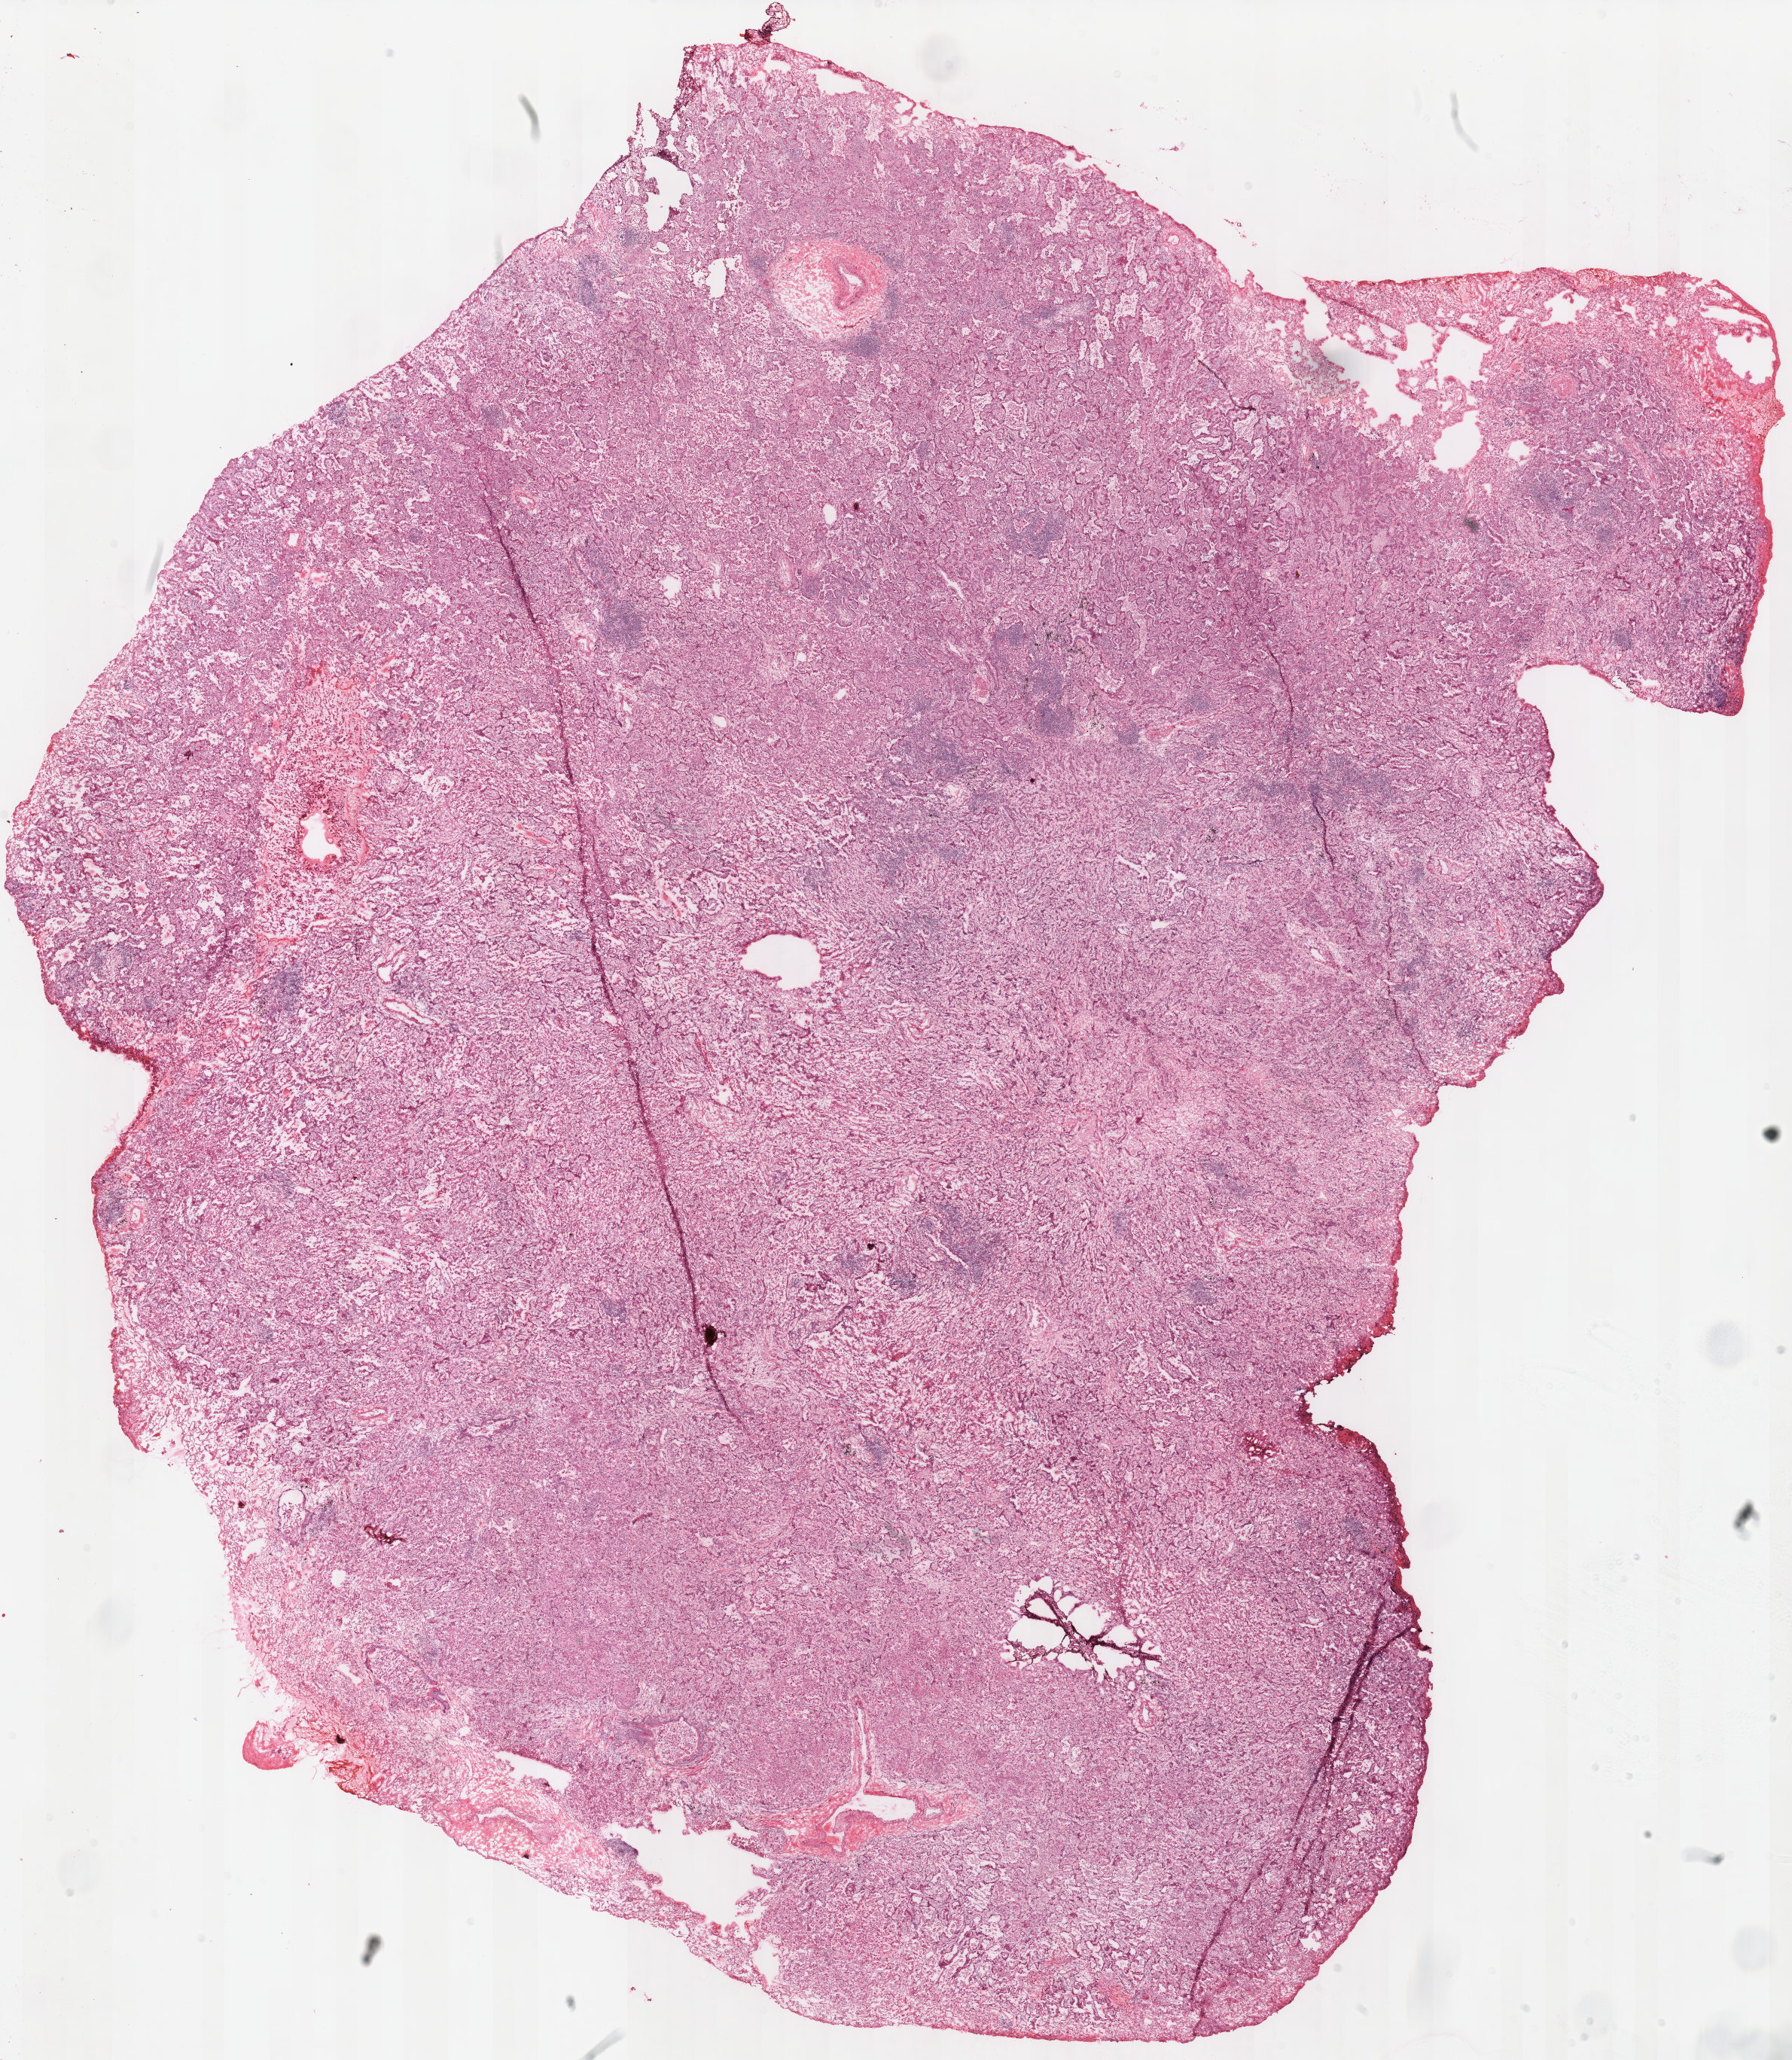
Hematoxylin and eosin (H&E) stained whole-slide image — whole scanned area (about 18.8 x 21.6 mm, slide scanned at 40x) shown as a low-resolution overview. Frozen section from the top of the tissue portion. Lung, primary tumour sample. Patient: female, age at initial diagnosis 61 years. Pathologist review of this section (percent, as recorded): tumour cells 100%, tumour nuclei 65%, normal cells 0%, stromal cells 0%, necrosis 0%. Infiltration values recorded for this section: lymphocyte infiltration 20%, monocyte infiltration 0%, neutrophil infiltration 5%.
* AJCC pathologic stage: IA
* laterality: left
* TNM: T1b N0 M0
* pathologic diagnosis: Bronchio-alveolar carcinoma, mucinous (lower lobe, lung)